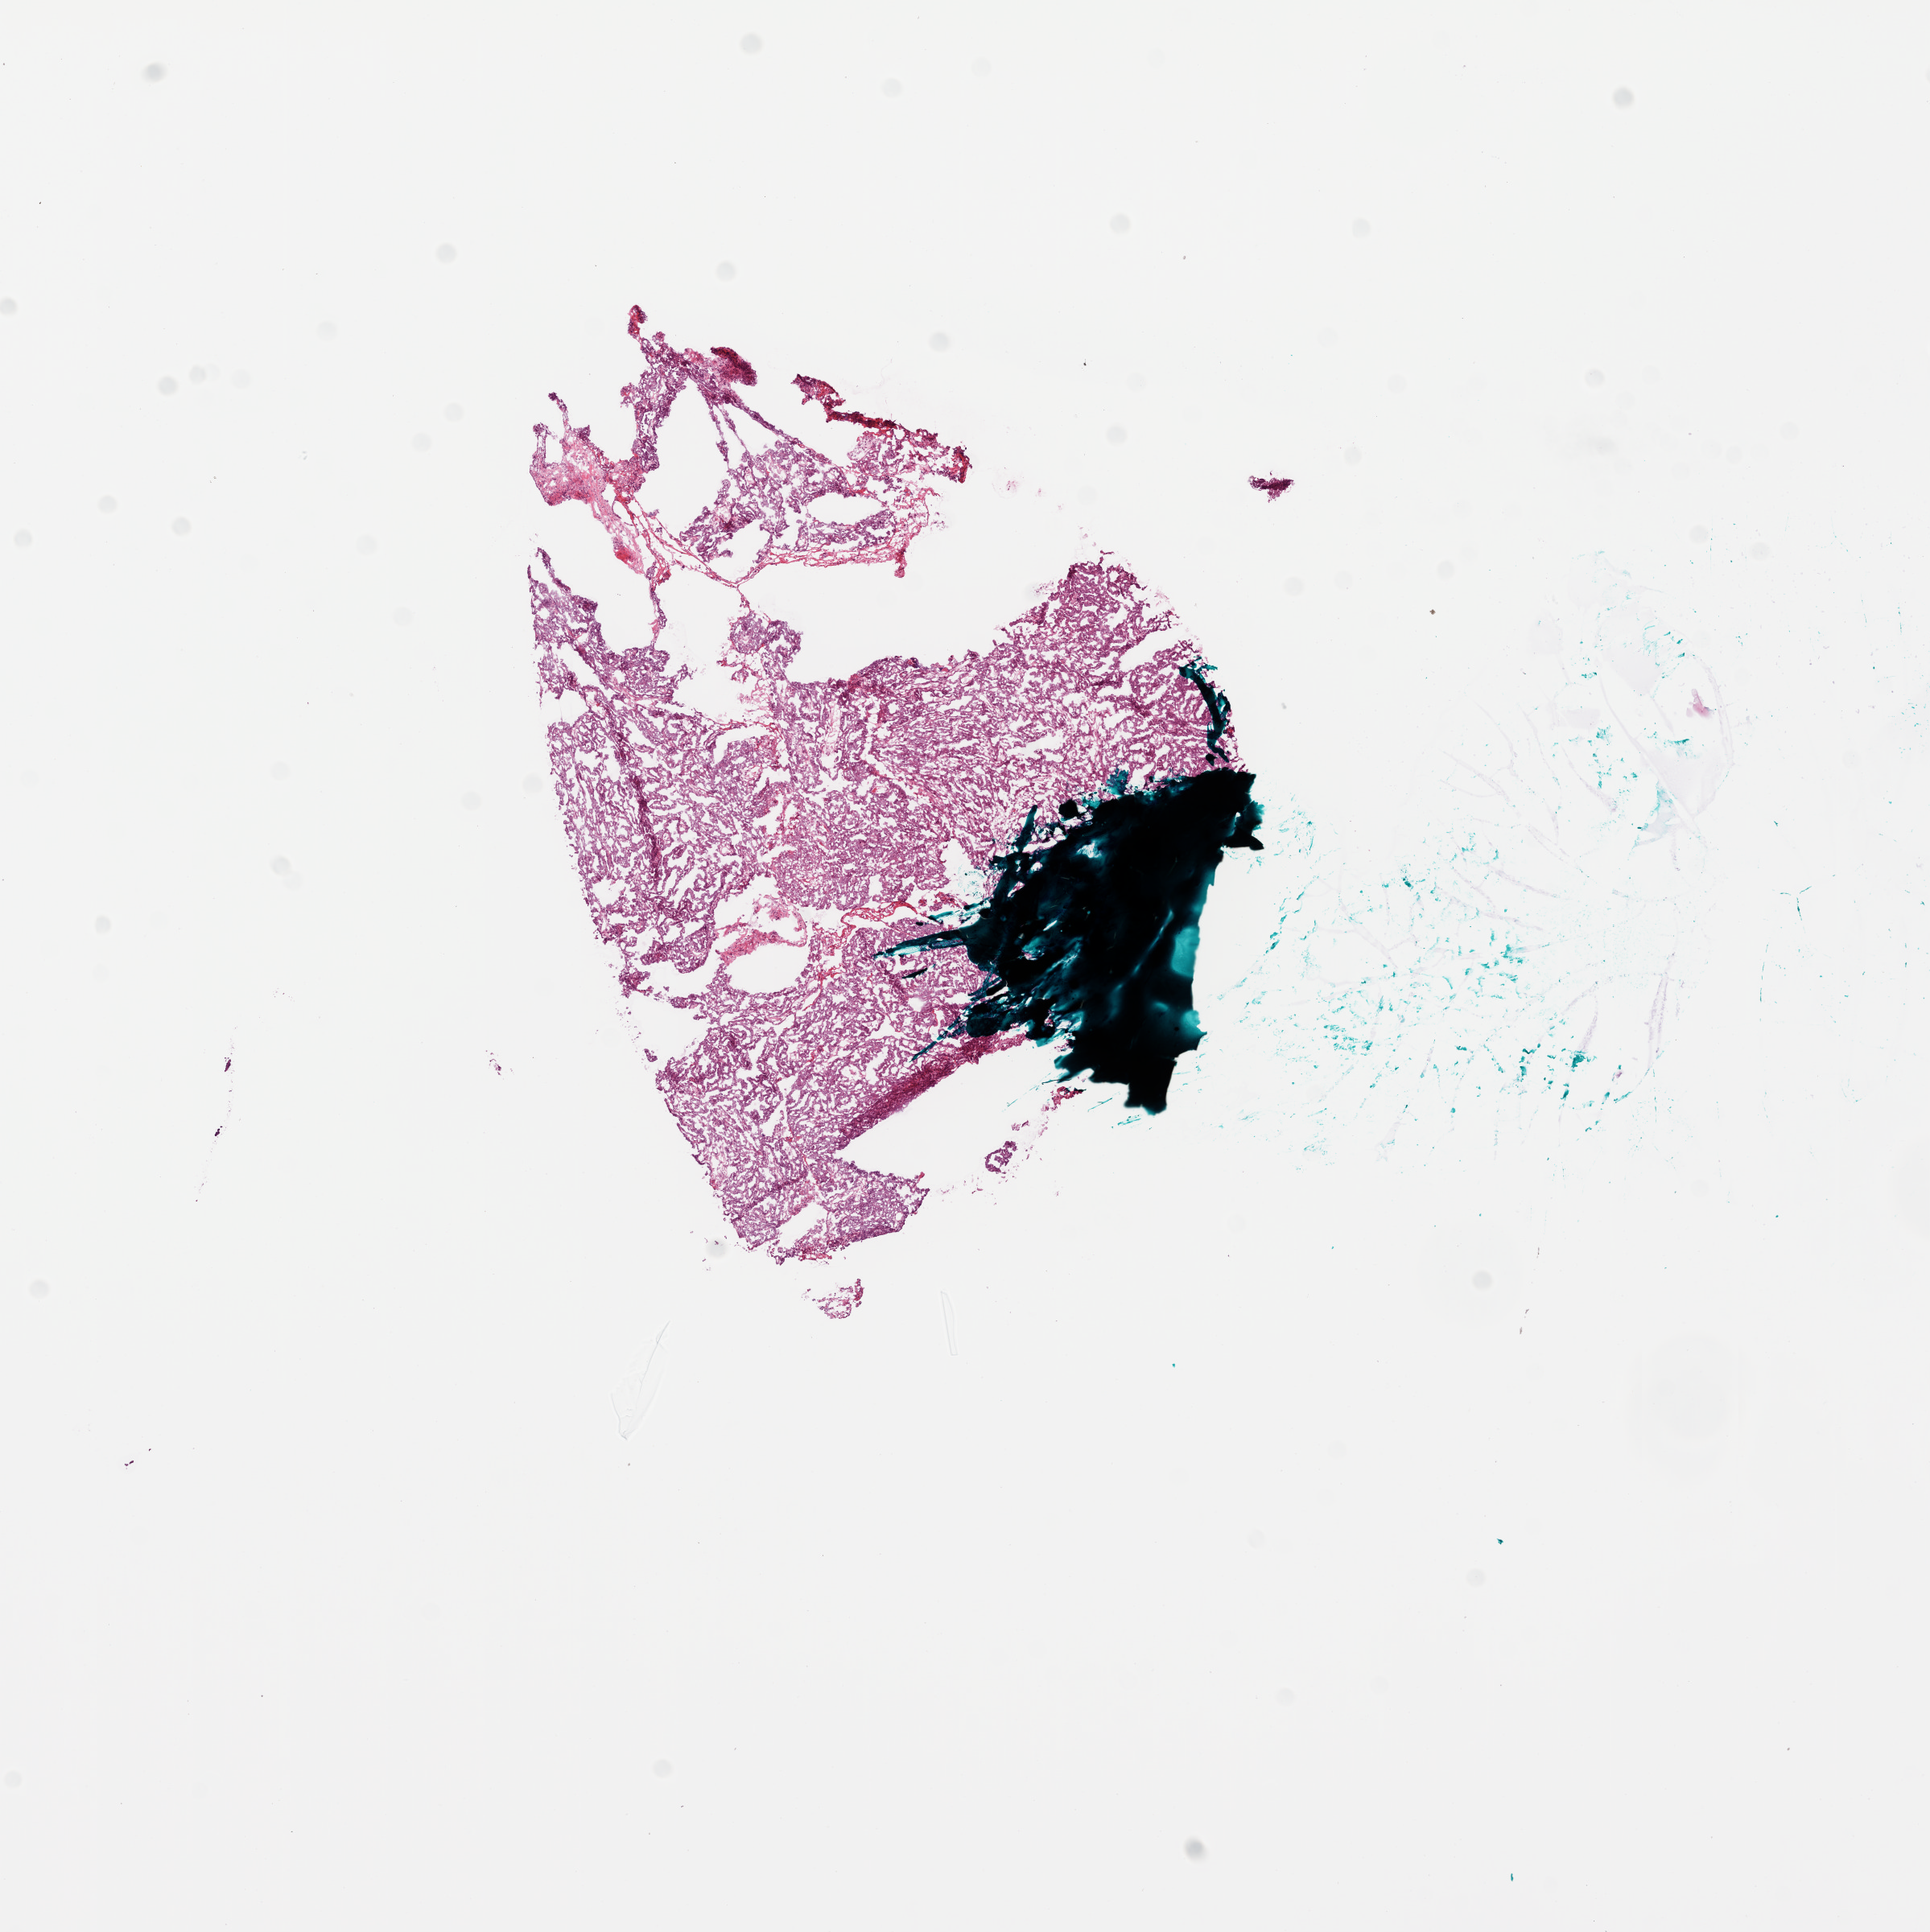
Whole-slide histology image, H&E — a low-resolution overview of the entire scanned area, about 9.7 x 9.7 mm (from a 20x scan), frozen section, primary tumour sample from the ovary. Female, age 64 years at initial diagnosis. Histologic grade: G3 (poorly differentiated). Pathologist review of this section (percent, as recorded): tumour cells 95%, tumour nuclei 95%, normal cells 5%, stromal cells 0%, necrosis 0%.
Histologic diagnosis: Serous cystadenocarcinoma, NOS. FIGO stage: IIIC. Laterality: left.